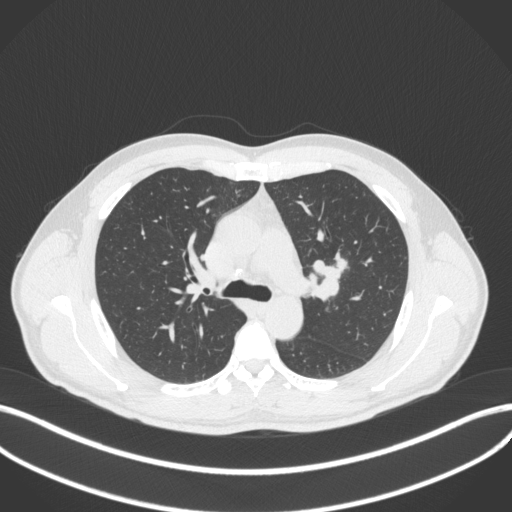
Chest CT, one axial slice. Slice 278 of 383 in the series (ordered by position). Reconstruction kernel B31f. 120 kVp. Lung window (W 1500 / L -600 HU). 512 × 512 image matrix. Male patient, age 50 years. From the clinical record (not read from this slice): clinical TNM (as recorded): T1c N1 M1b.
Structures marked on this image (rectangle marked by the reading radiologist):
- lung tumour (recorded histology: squamous cell carcinoma): bounding box [x1, y1, x2, y2] px = [310, 251, 349, 301]